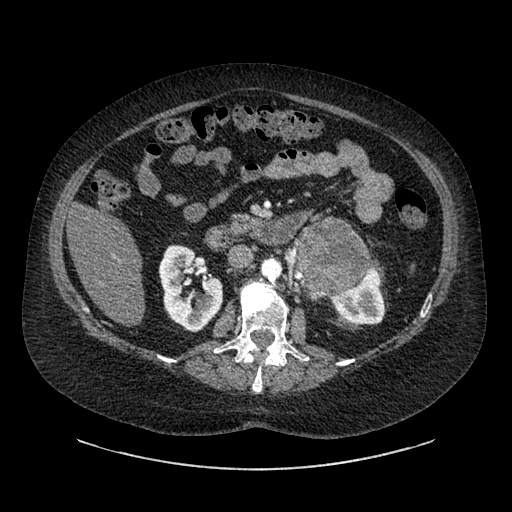
Contrast-enhanced abdominal CT, one axial slice; slice 515 of 769 in the series (ordered by position); reconstruction kernel SOFT; 120 kVp; intravenous contrast given; soft-tissue window (W 400 / L 40 HU); 0.62 mm slice thickness; 512 × 512 image matrix, field of view 460 × 460 mm. Female patient, age 61 years. Case-level facts recorded for this patient, not image findings: diagnosis: adrenocortical carcinoma; tumour side: left adrenal; tumour size at pathology: 13 cm; Ki-67 index: 79 %; stage (as recorded): 2.
Outlined on this slice (semi-automatically segmented with operator editing):
- mass: box from (x=297, y=222) to (x=369, y=293) px